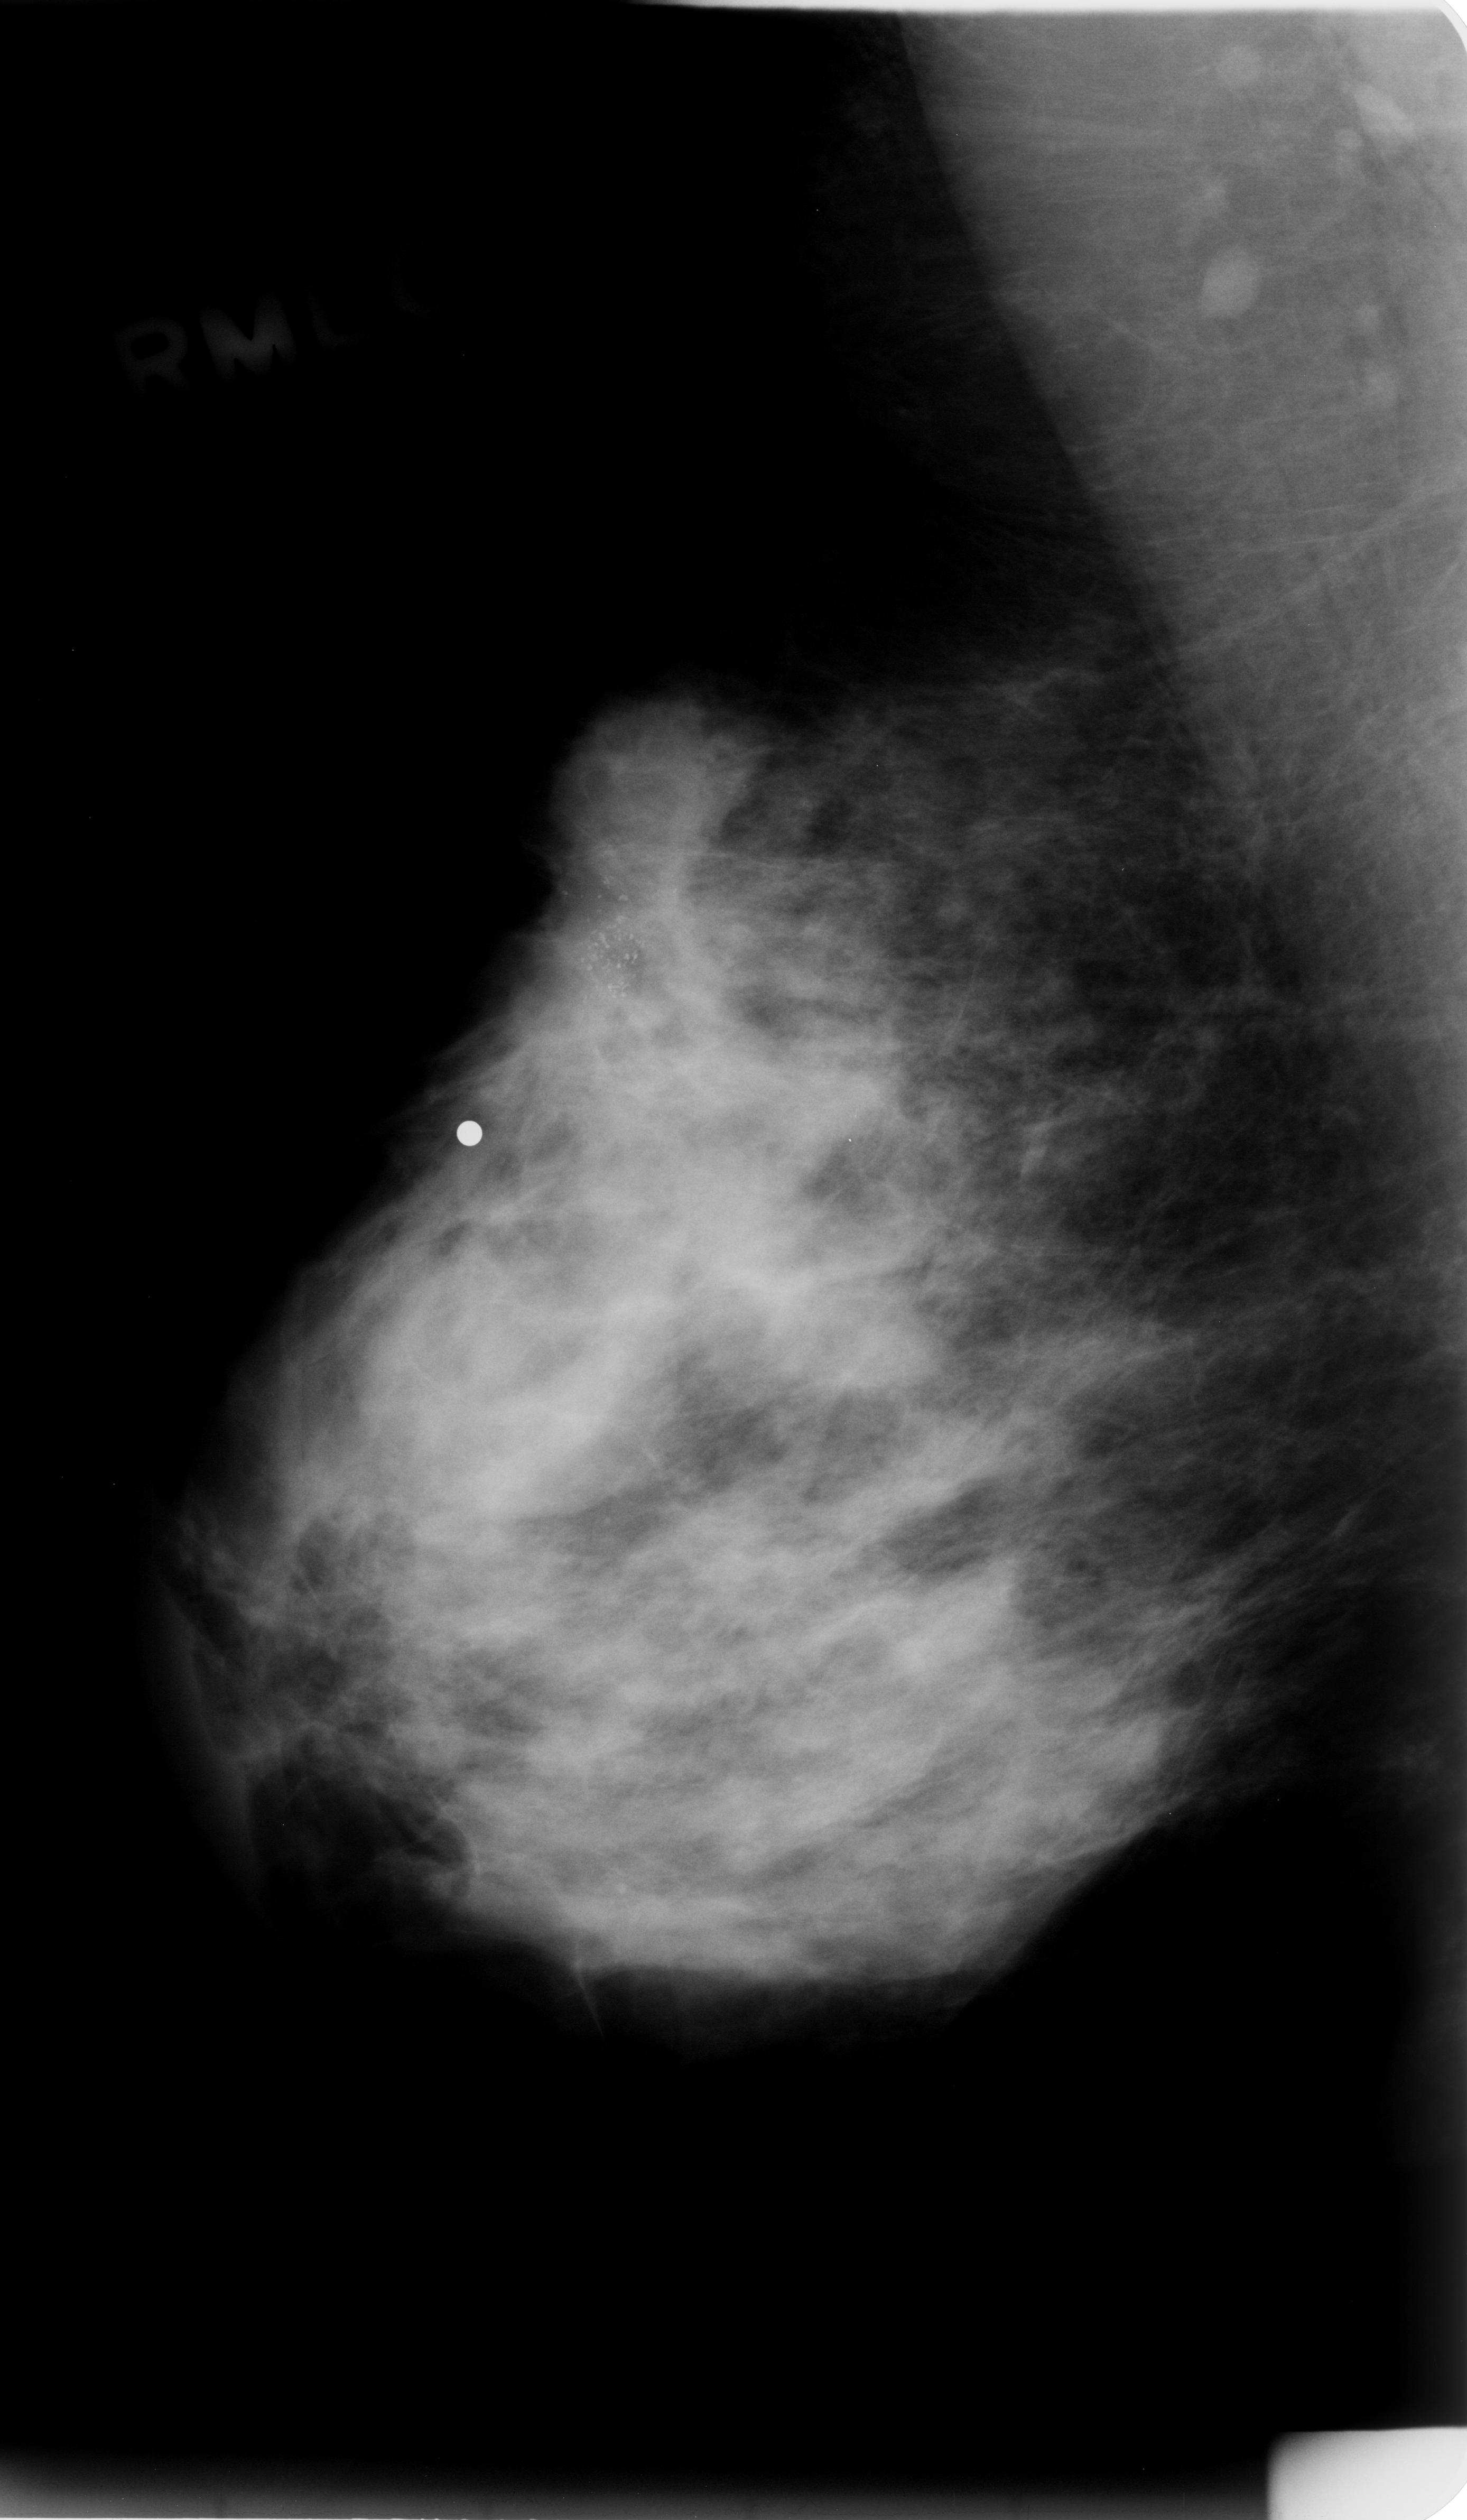
Mammogram (digitized film); right breast; MLO view.
- Marked abnormality: calcifications, morphology pleomorphic, distribution clustered; BI-RADS assessment category 5; pathology result (as recorded, not read from the image): malignant.